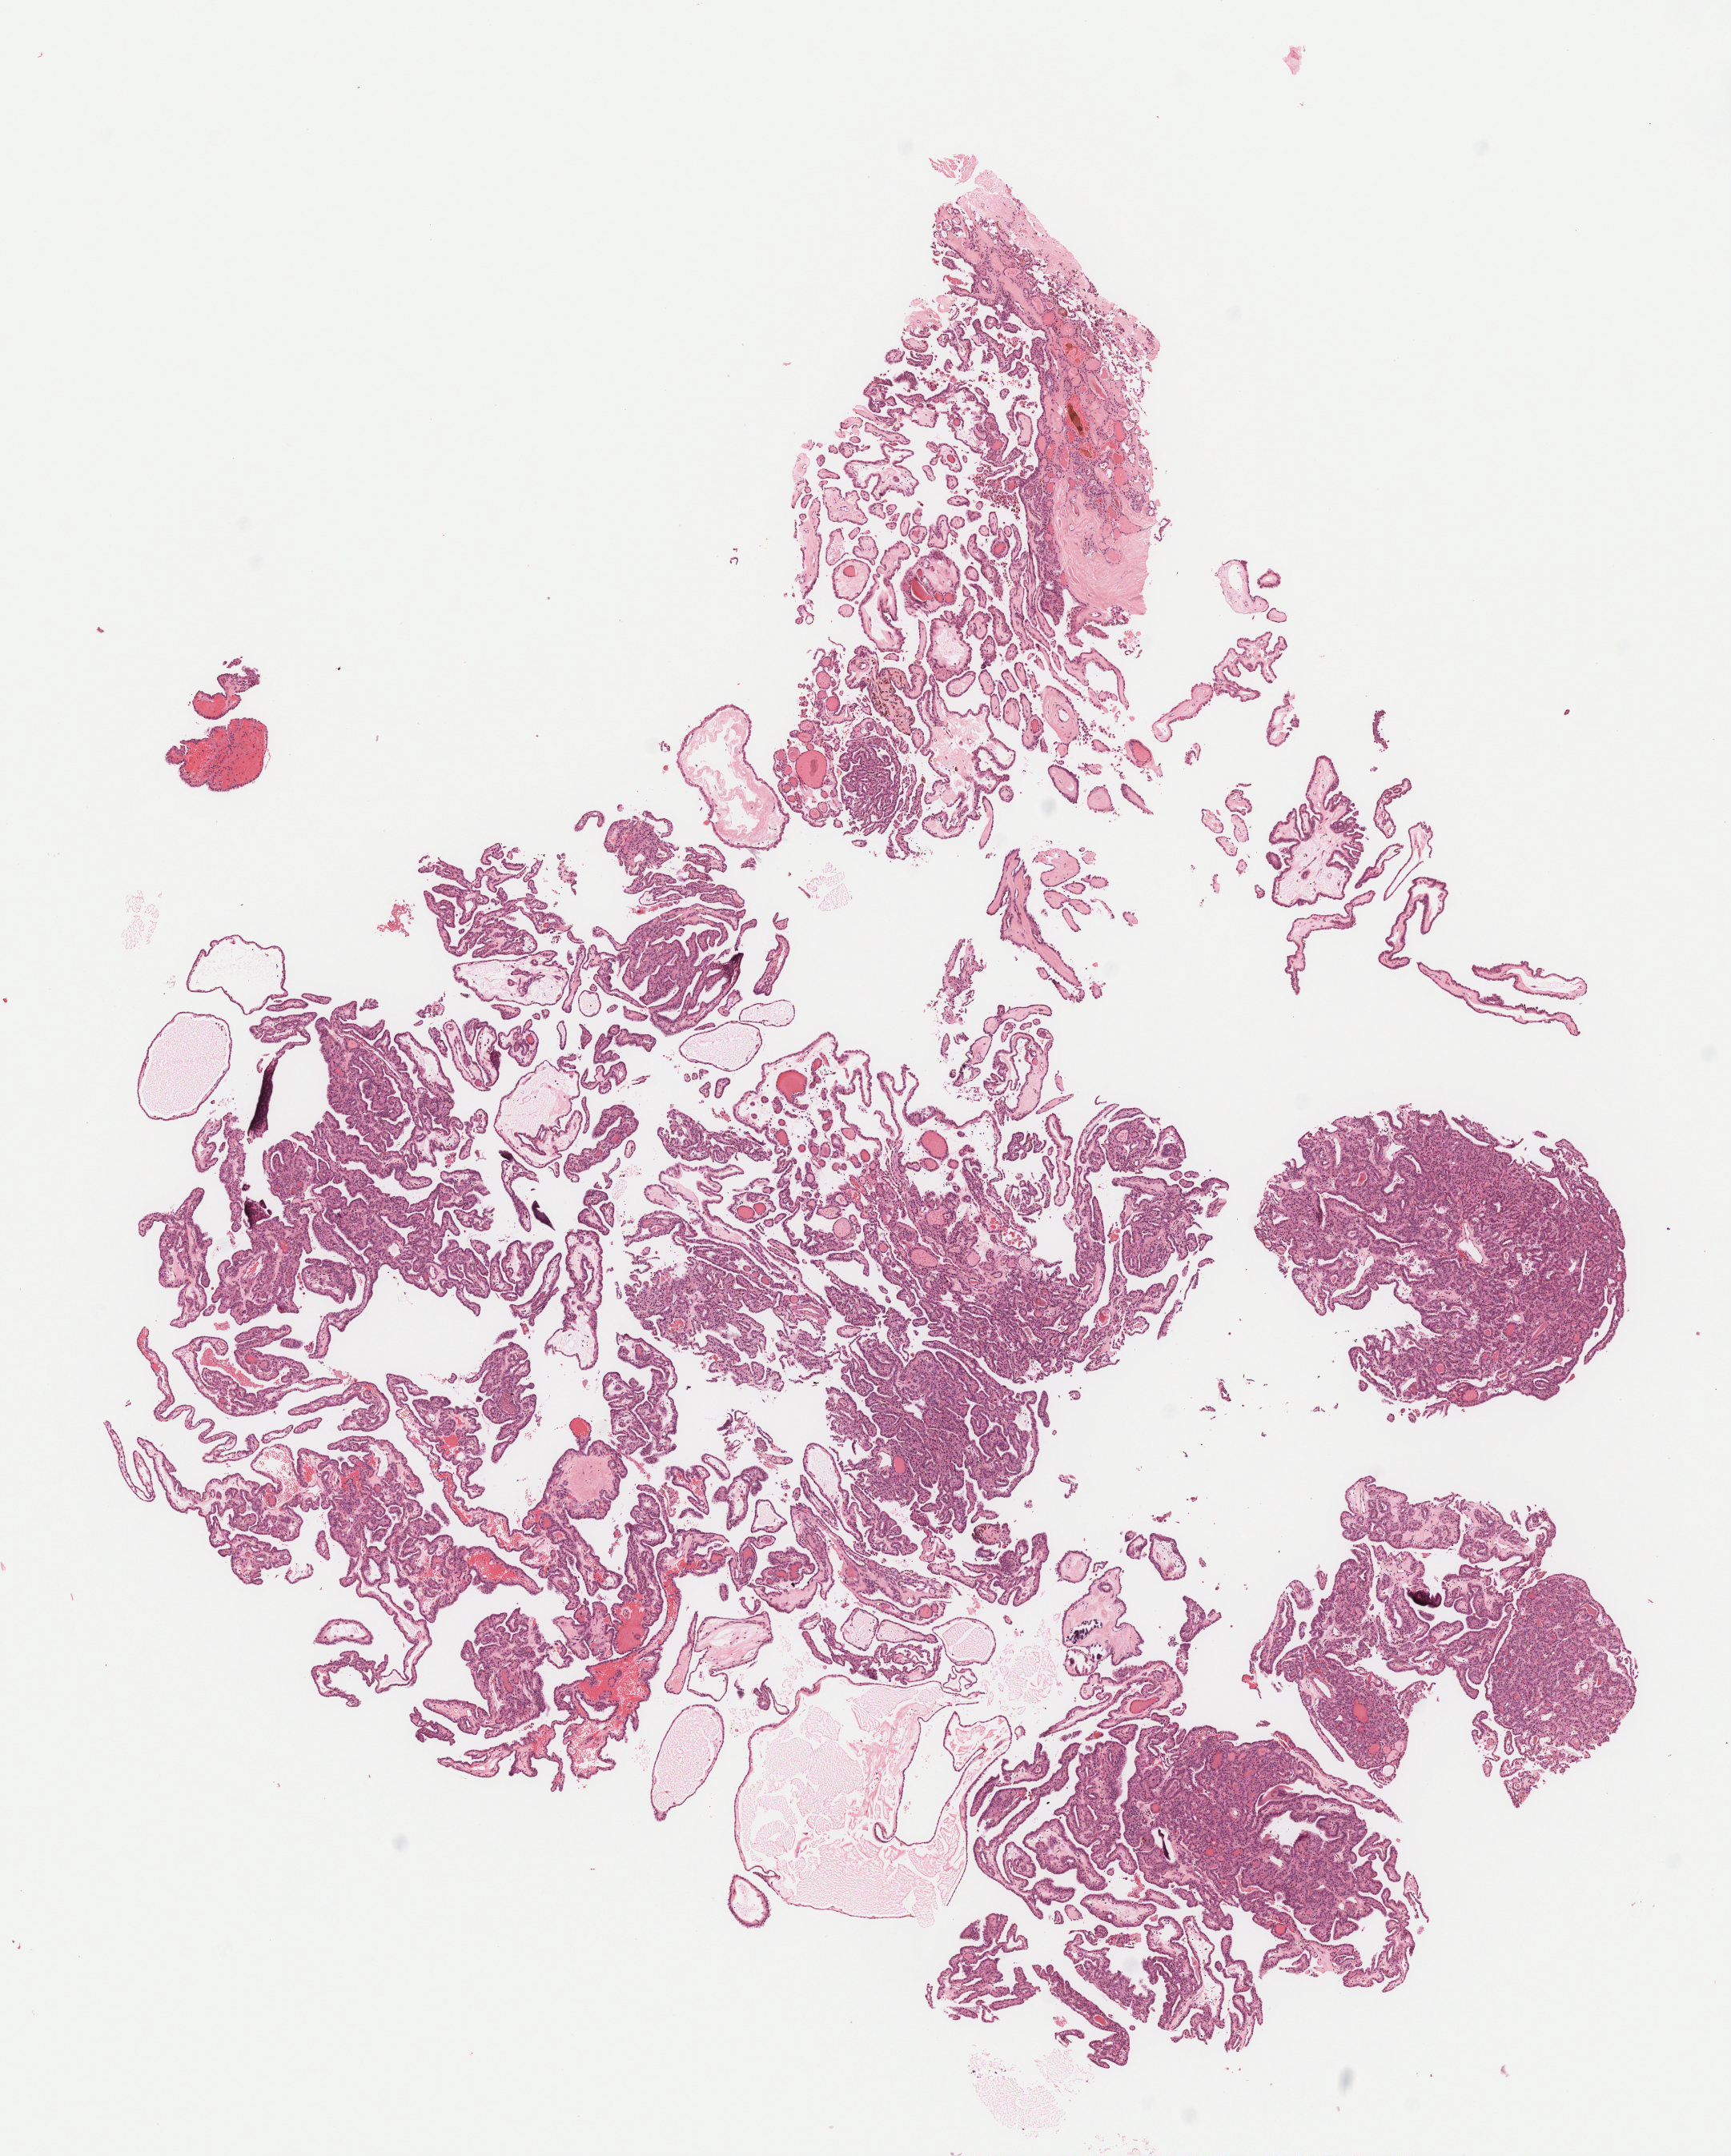
Digitized H&E-stained tissue section (whole slide) — whole scanned area (about 8.7 x 10.8 mm) shown as a low-resolution overview. Formalin-fixed paraffin-embedded (FFPE) diagnostic section. Primary tumour sample from the thyroid. Male, age 66 years at initial diagnosis.
Laterality: midline. AJCC pathologic stage: I (7th edition). Diagnosis: Papillary adenocarcinoma, NOS (thyroid gland). Lymph nodes positive (case pathology): 0 of 2 examined.